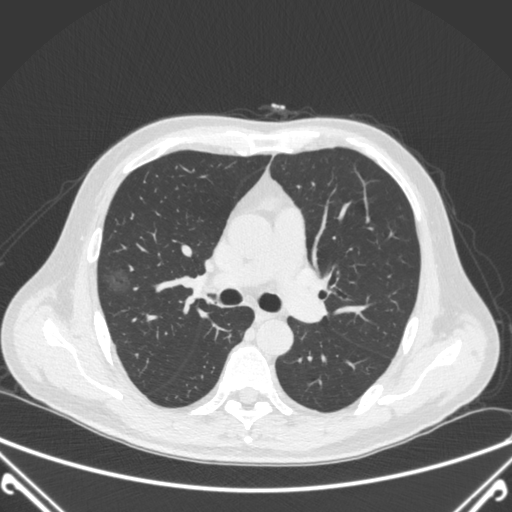
Chest CT, one axial slice. Position 227 of 360 along the scan axis. 120 kVp. Lung window (W 1500 / L -600 HU). 1 mm slice thickness. 512 × 512 image matrix, field of view 380 × 380 mm. Patient: male, 64 years. Case-level facts recorded for this patient, not image findings: clinical TNM (as recorded): T1c N0 M0; histopathological grade: G2.
Structures marked on this image (rectangle marked by the reading radiologist):
- lung tumour (recorded histology: adenocarcinoma): bounding box (x1, y1, x2, y2) in pixels: (100, 263, 140, 304)